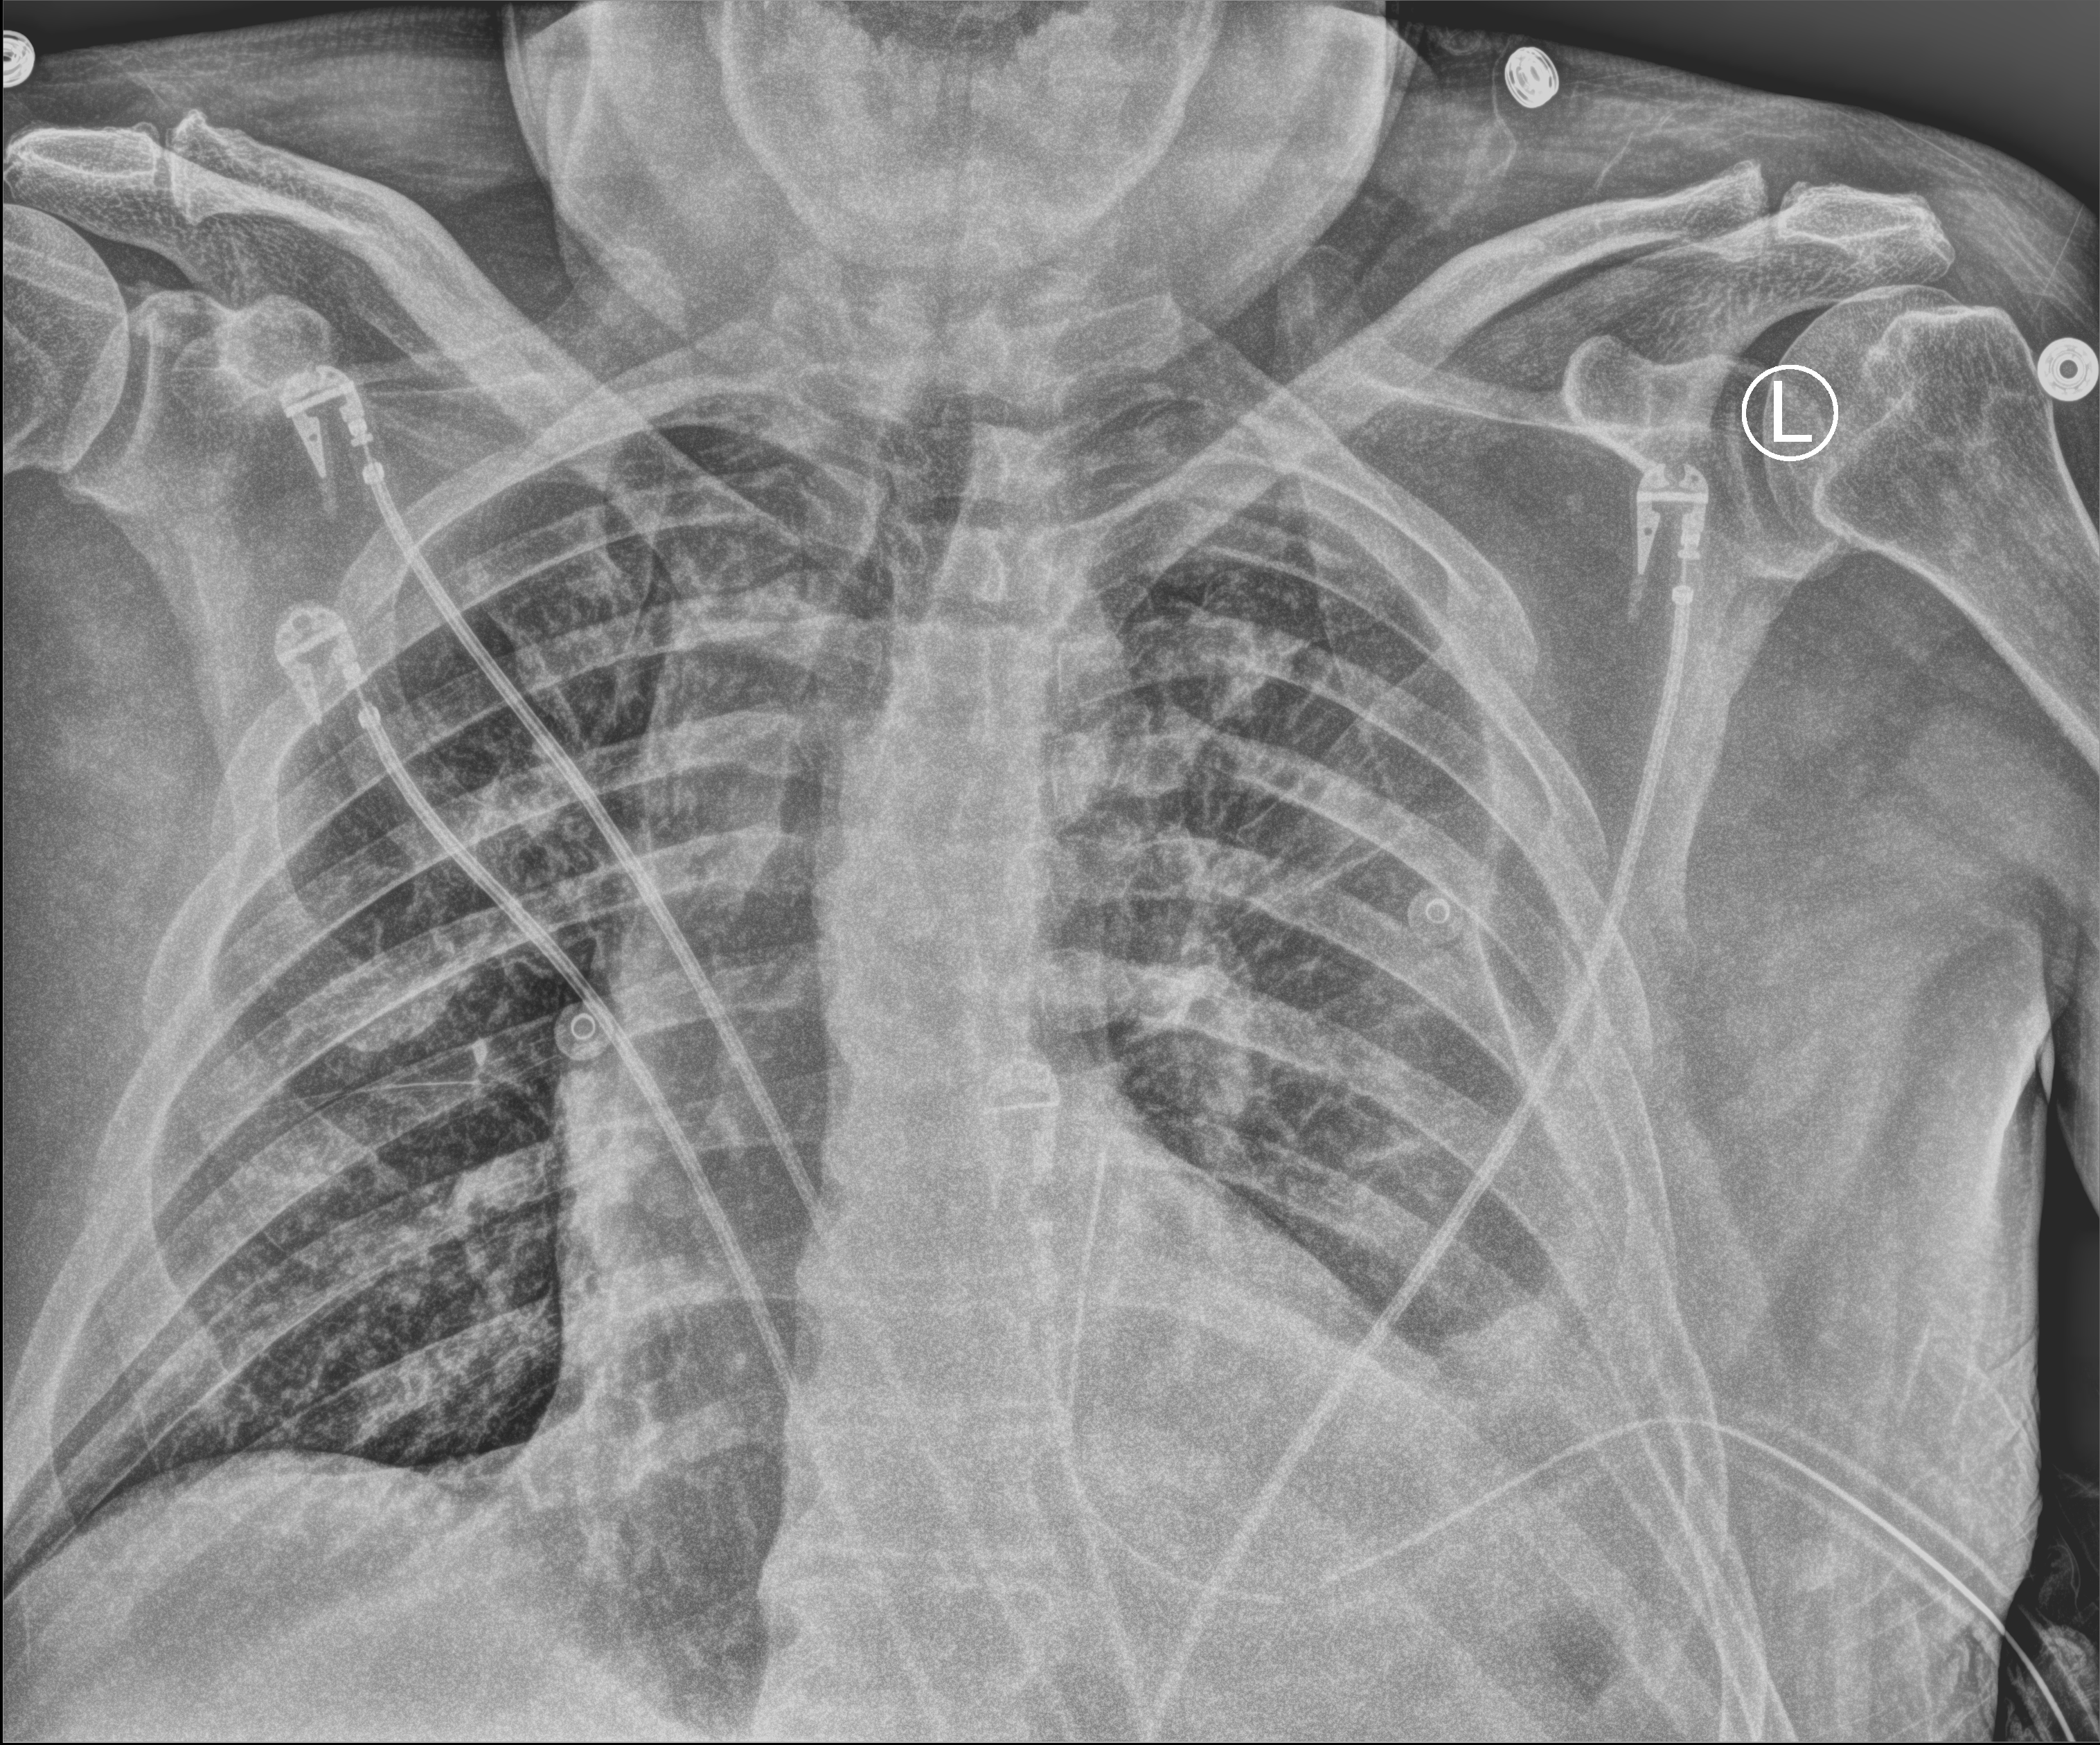
Bedside chest radiograph (computed radiography), anteroposterior (AP) projection. Patient hospitalised with COVID-19; male, aged 18–59 years.
Hospital-stay facts (about this admission, not read from this image; timing relative to this image not recorded): length of hospital stay: 10 days.